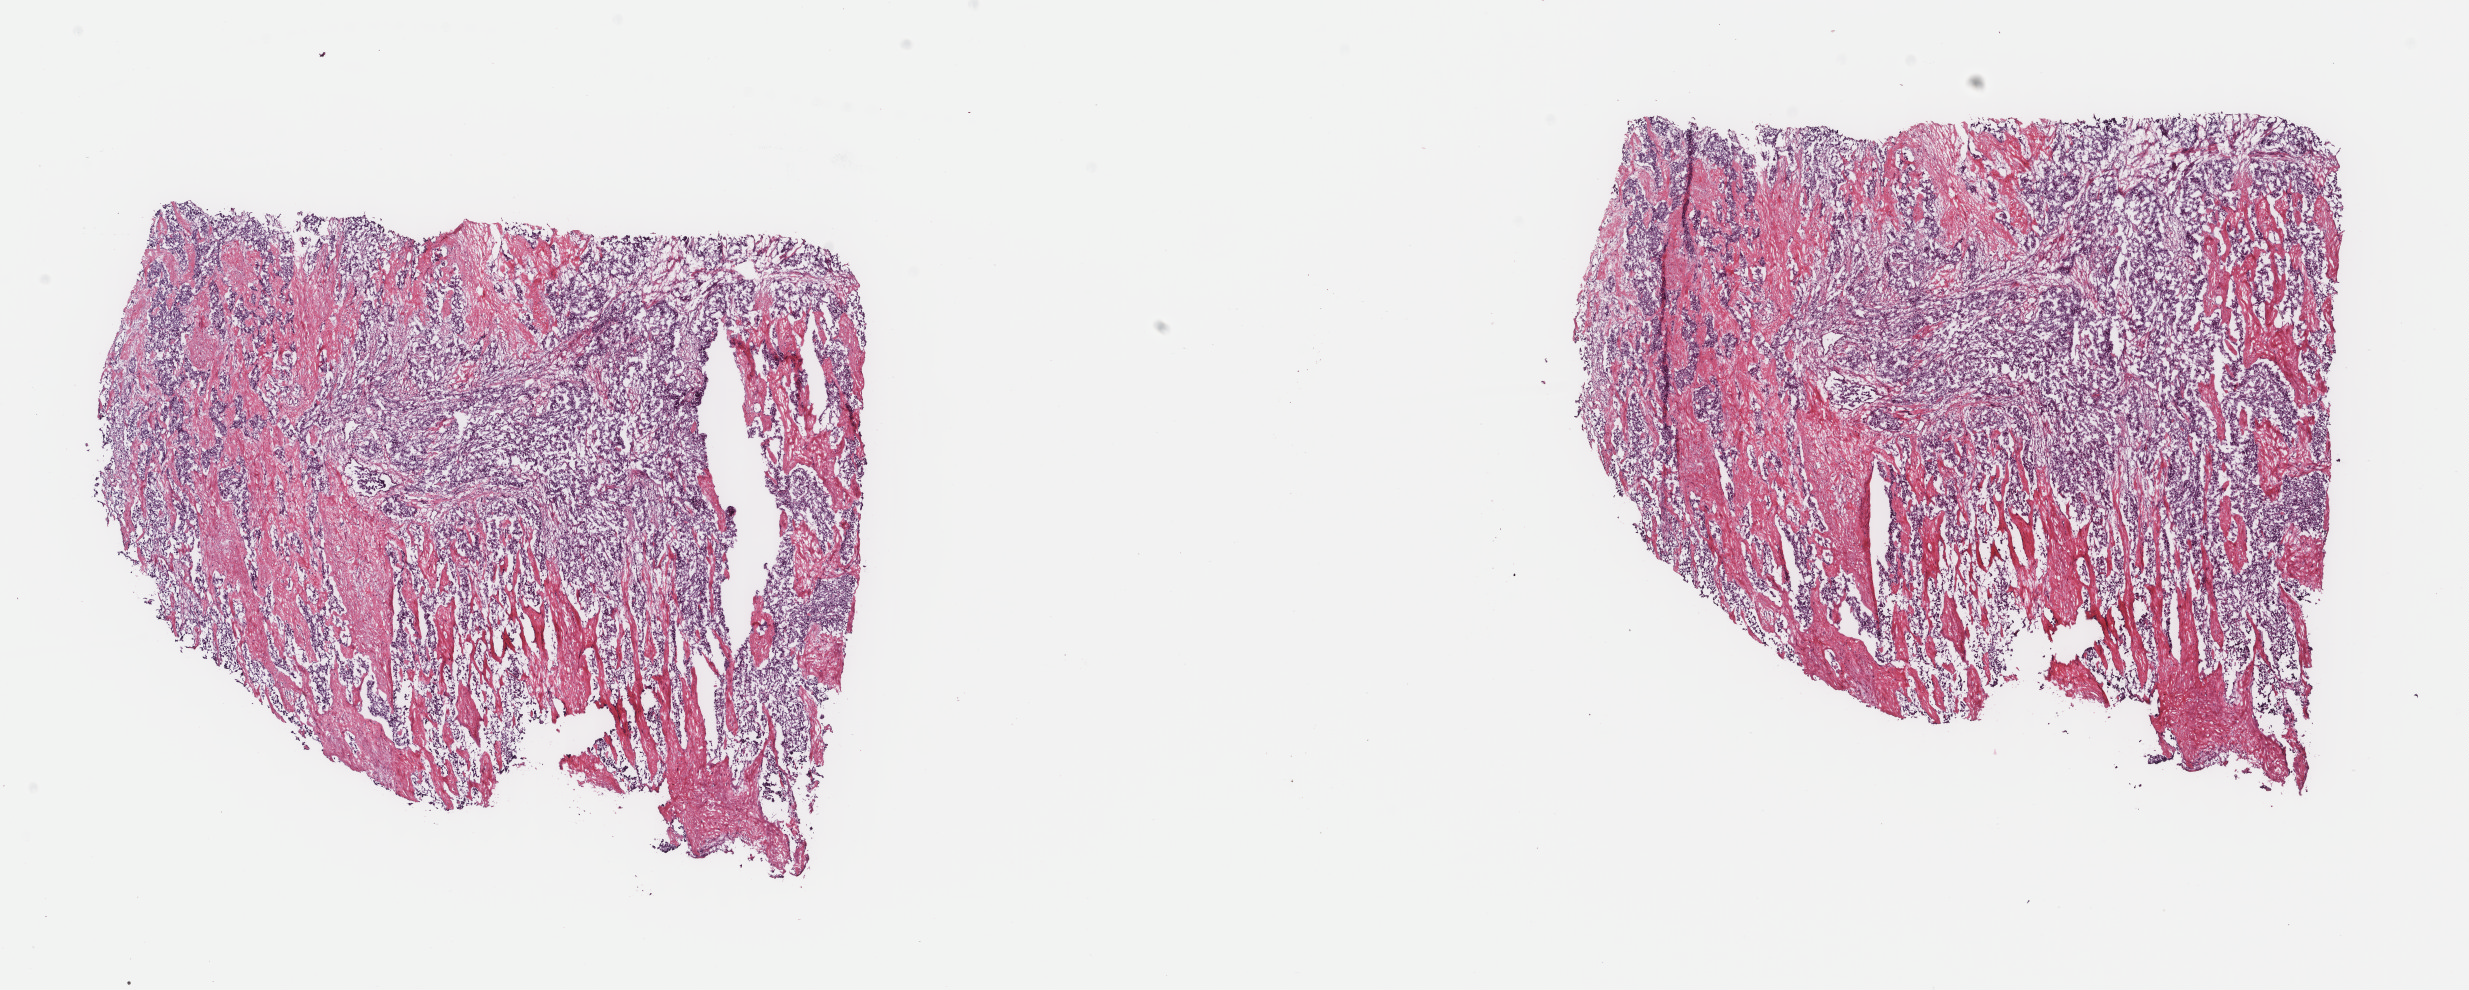
Hematoxylin and eosin (H&E) stained whole-slide image — shown as a low-resolution overview of the whole scanned area (about 19.6 x 7.9 mm), frozen section from the top of the tissue portion, sample: primary tumour, liver. Female patient; age at initial diagnosis 64 years. Histologic grade: G2 (moderately differentiated). Pathologist review of this section (percent, as recorded): tumour cells 70%, tumour nuclei 70%, normal cells 0%, stromal cells 30%, necrosis 0%. Inflammatory infiltration, as recorded: lymphocyte infiltration 2%, monocyte infiltration 0%, neutrophil infiltration 0%.
Histologic diagnosis: Hepatocellular carcinoma, NOS. AJCC pathologic stage: IVB (5th edition).